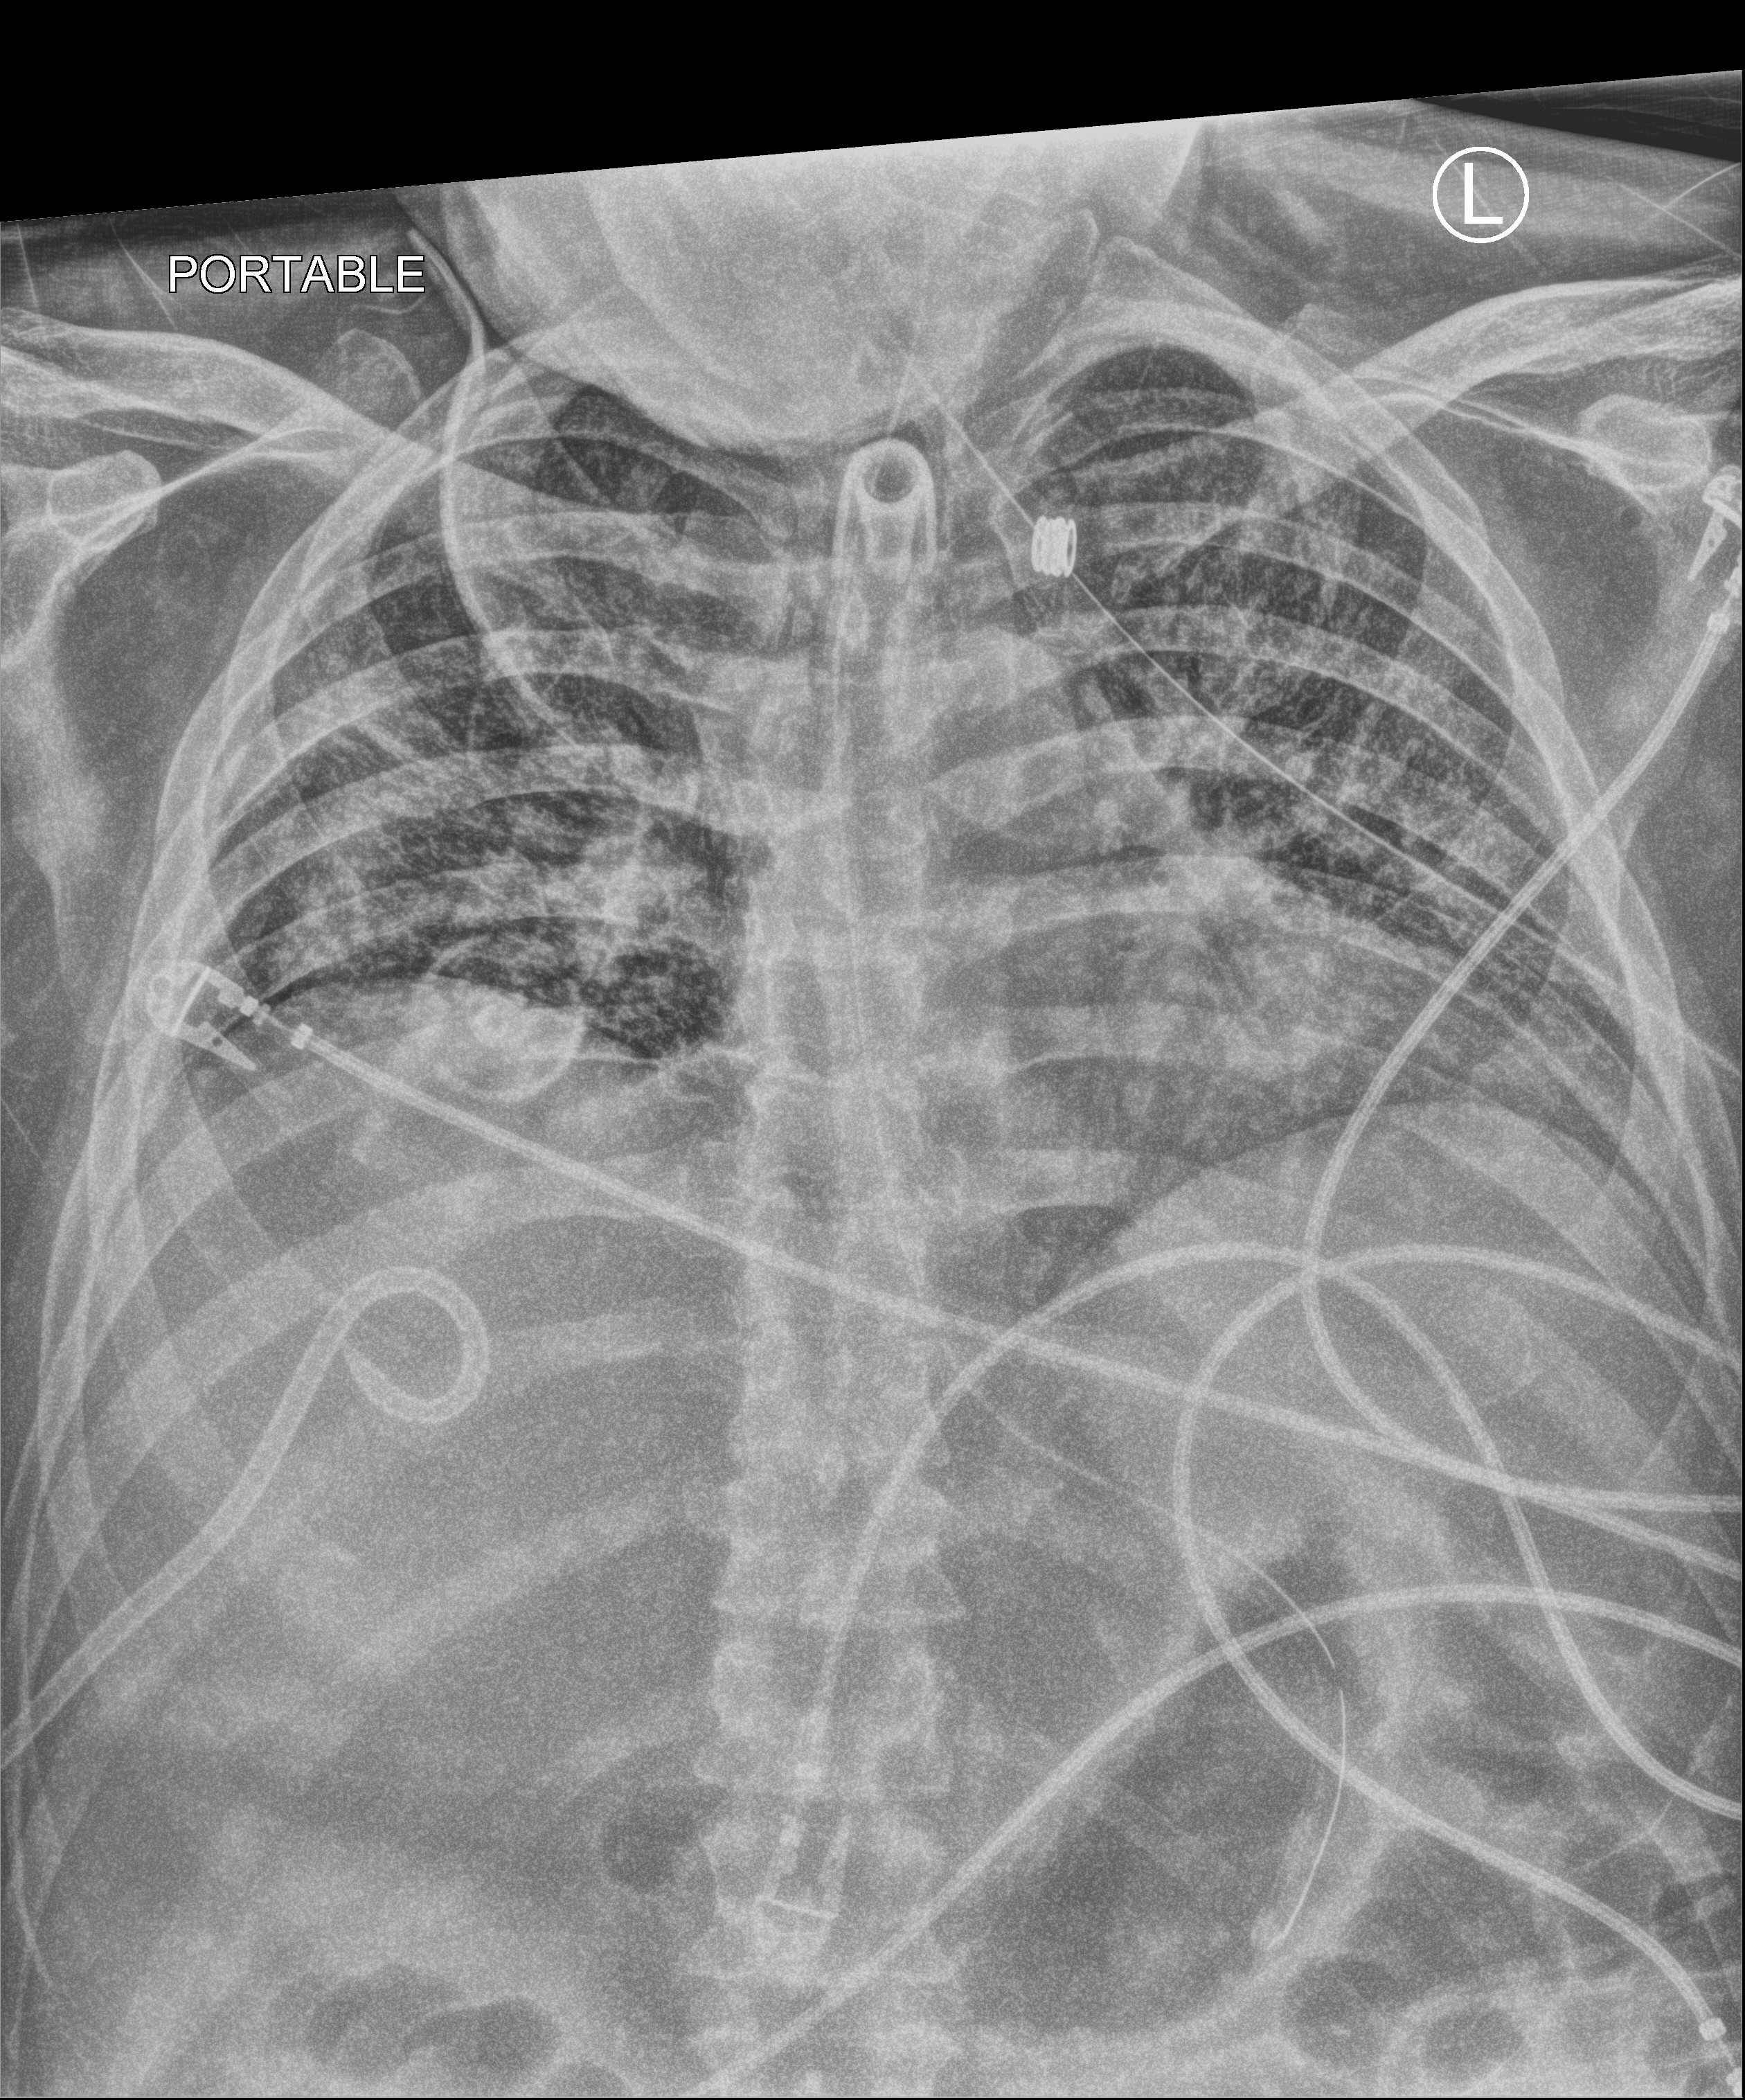
Bedside chest radiograph (computed radiography), anteroposterior (AP) projection. Male patient hospitalised with COVID-19, age 18–59 years.
Admission-level facts for this patient (not findings on this image; timing relative to this image not recorded):
- admitted to intensive care during this hospital stay: yes